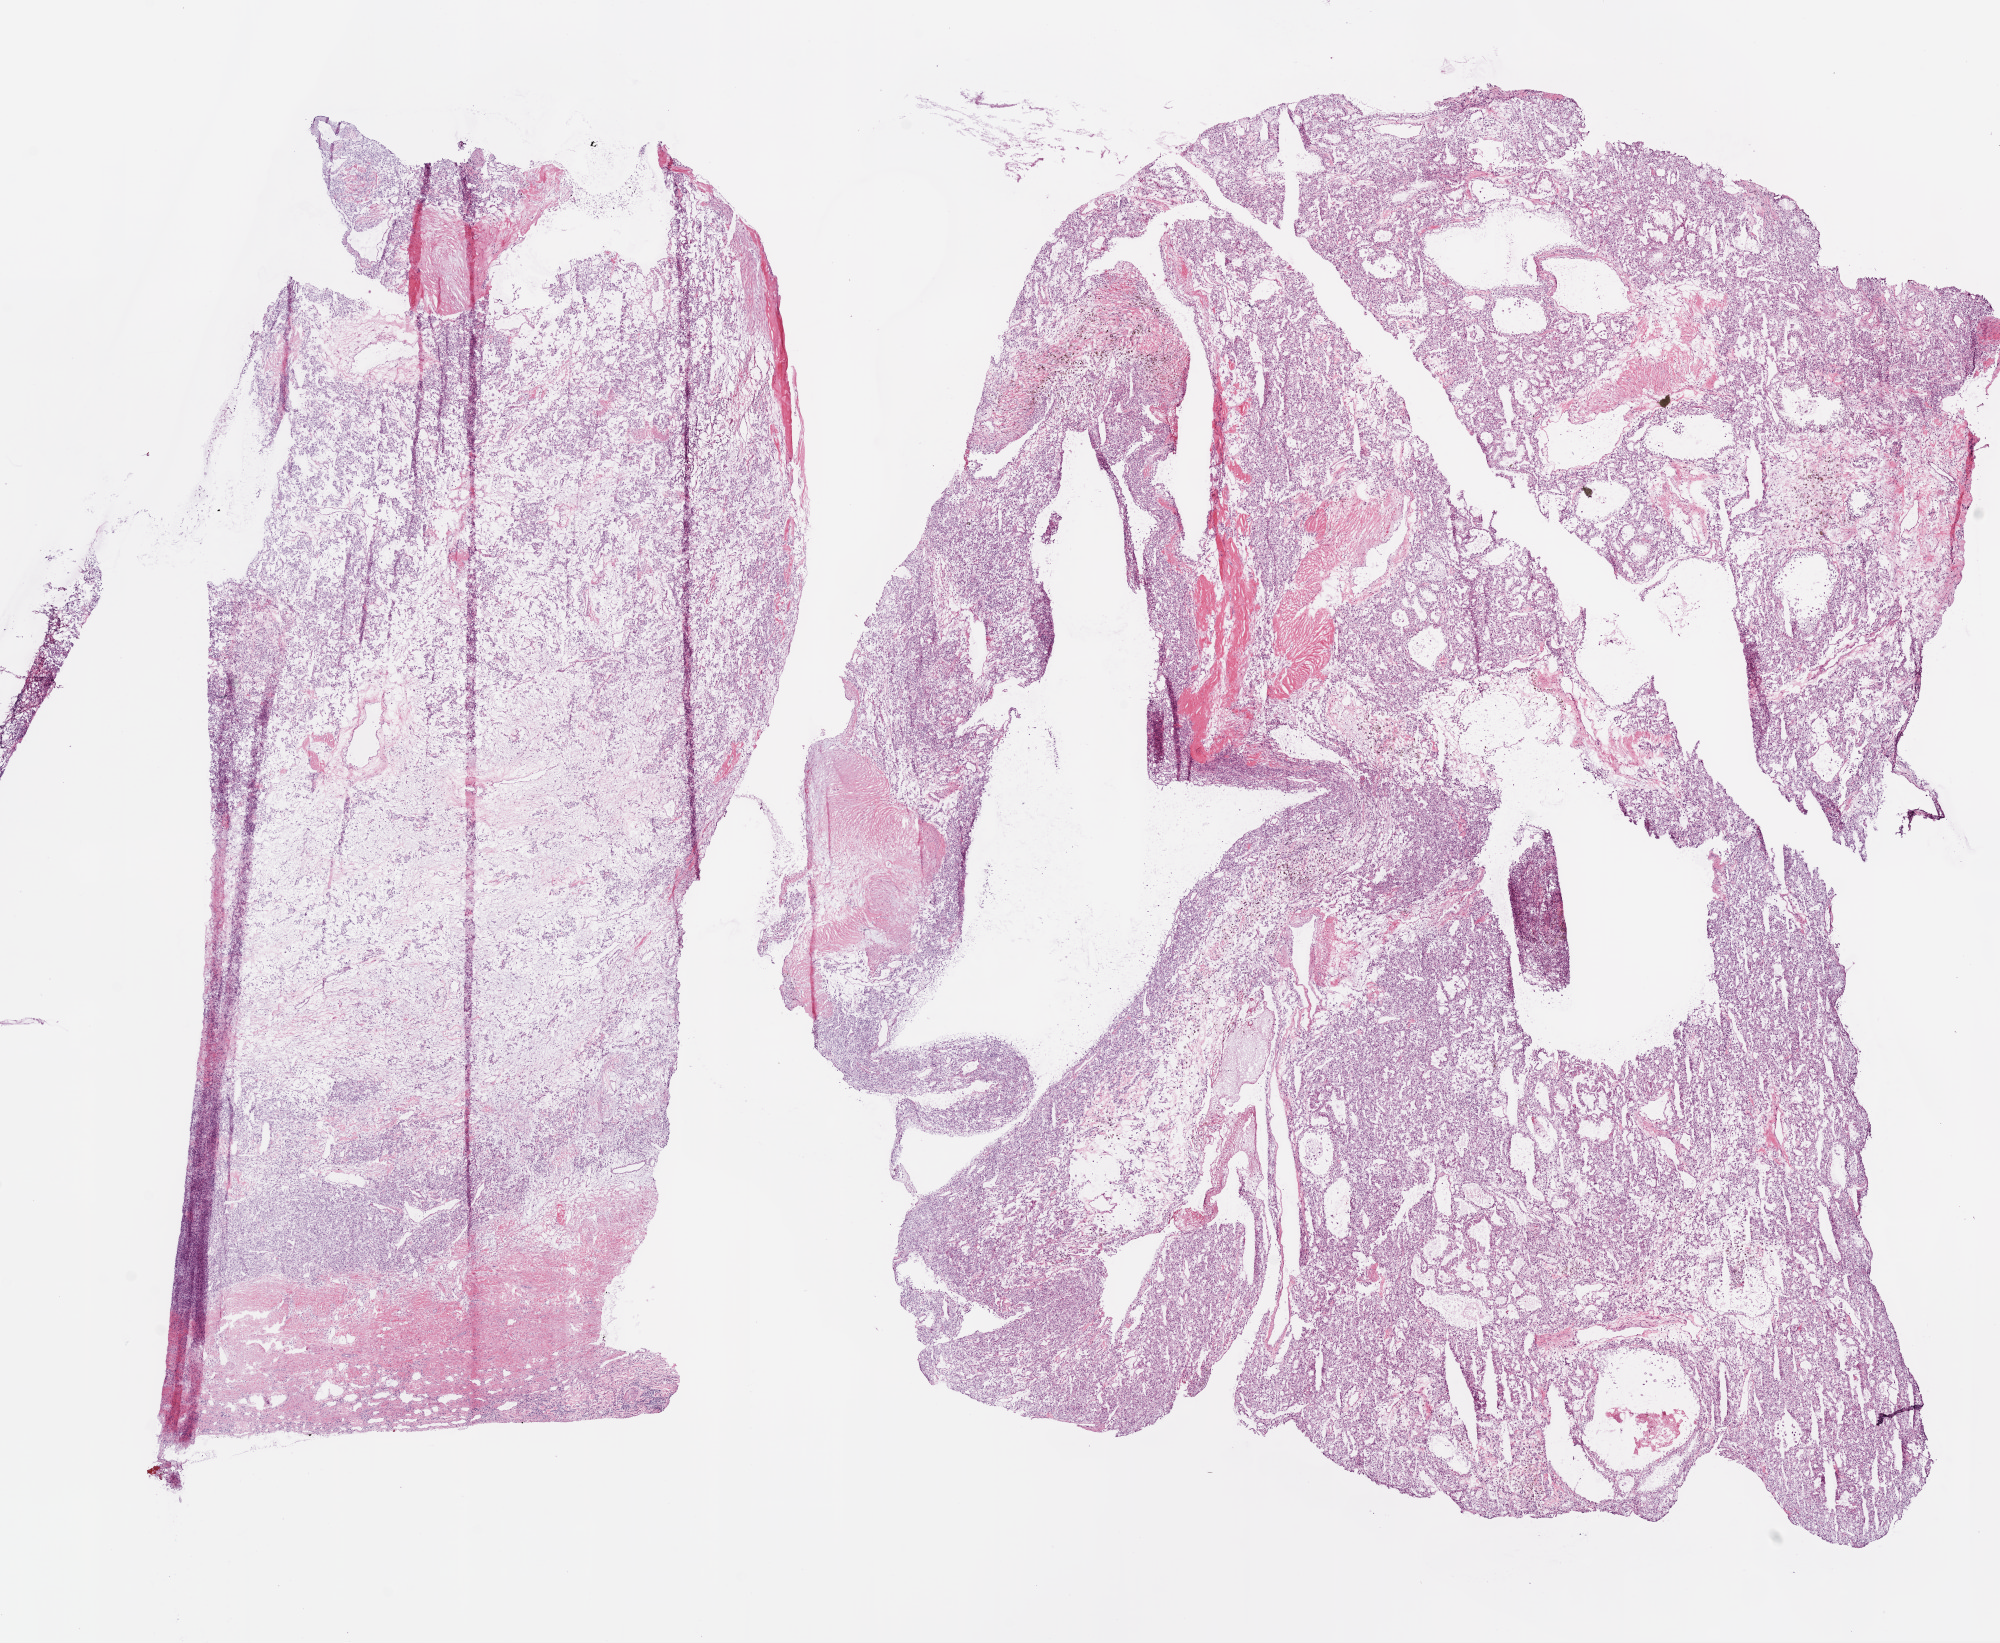
Digitized H&E tissue section (whole slide), whole scanned area (about 16.0 x 13.2 mm, slide scanned at 20x) shown as a low-resolution overview. Frozen section from the bottom of the tissue portion. Kidney, primary tumour sample. Male patient; age at initial diagnosis 49 years. Histologic grade: G3 (poorly differentiated). Composition of this section per pathologist review: tumour cells 70%, tumour nuclei 80%, normal cells 0%, stromal cells 30%, necrosis 0%.
AJCC pathologic stage: I. Pathologic diagnosis: Clear cell adenocarcinoma, NOS. Laterality: right. TNM: T1a NX M0.